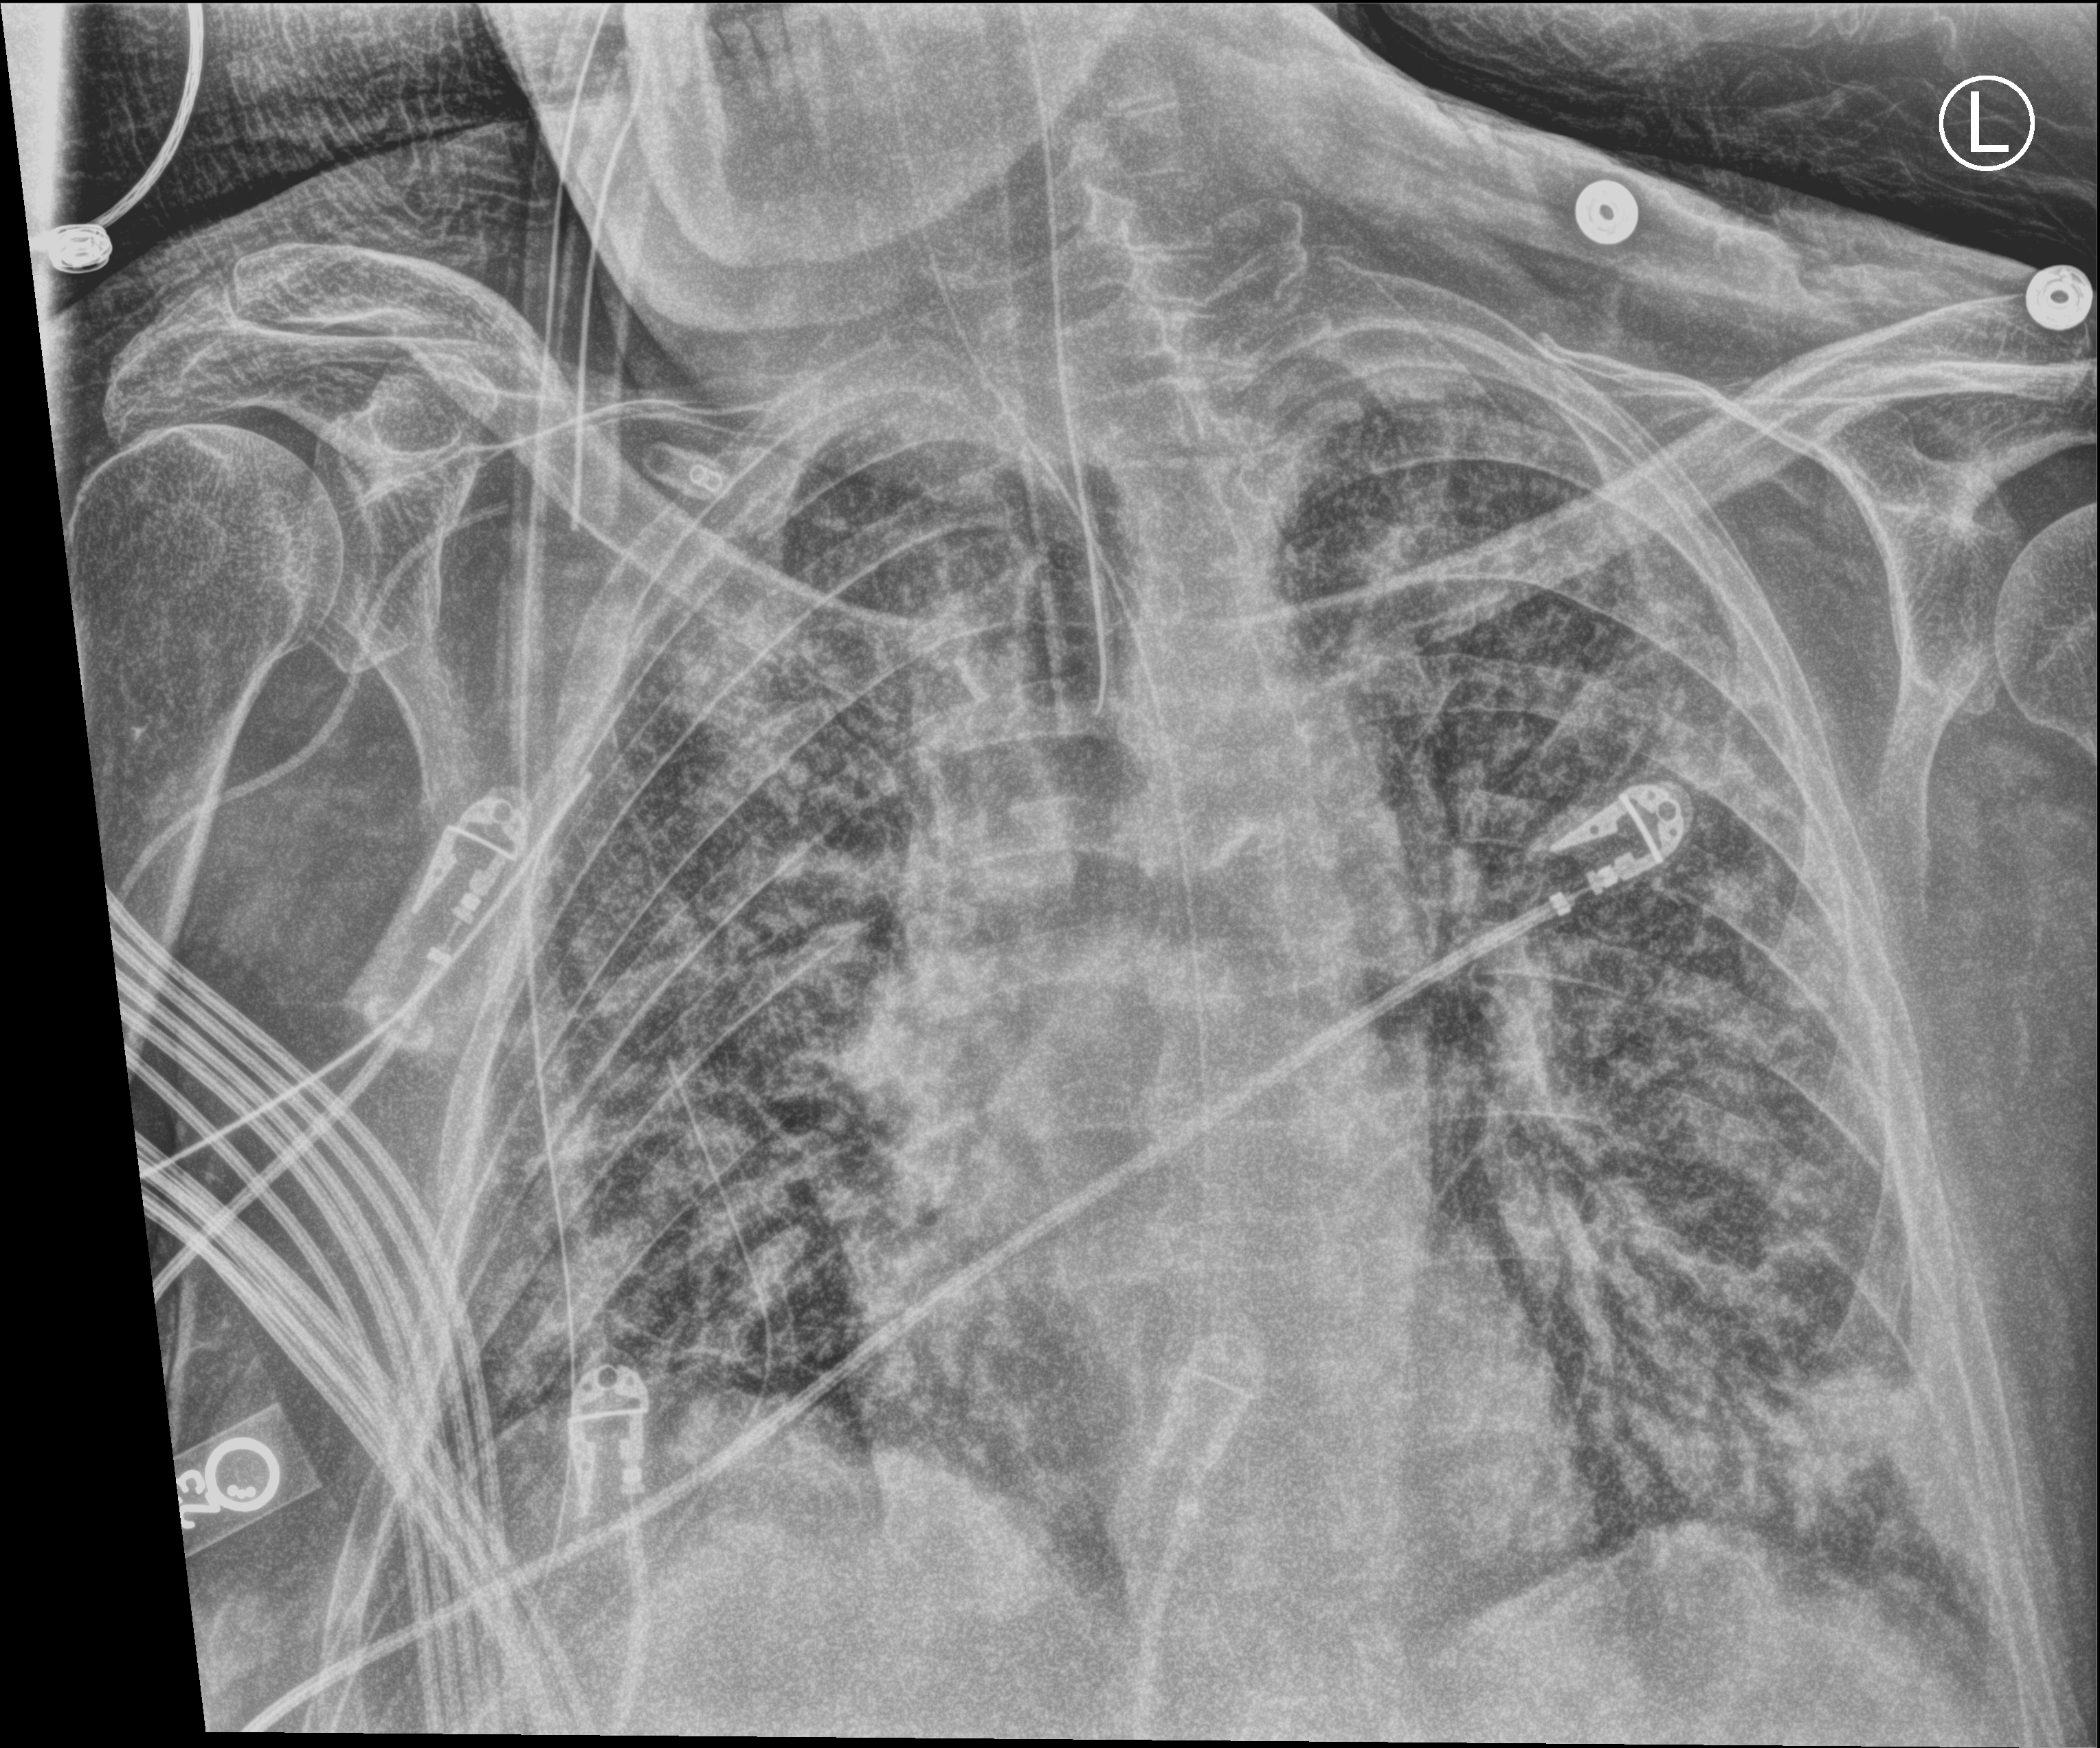
Portable chest radiograph; anteroposterior (AP) projection. Male patient hospitalised with COVID-19, age 60–74 years.
From the hospital-stay record, not from the radiograph (when in the stay this image was taken is not recorded): other chronic lung disease (admission record): no; COPD (admission record): no.